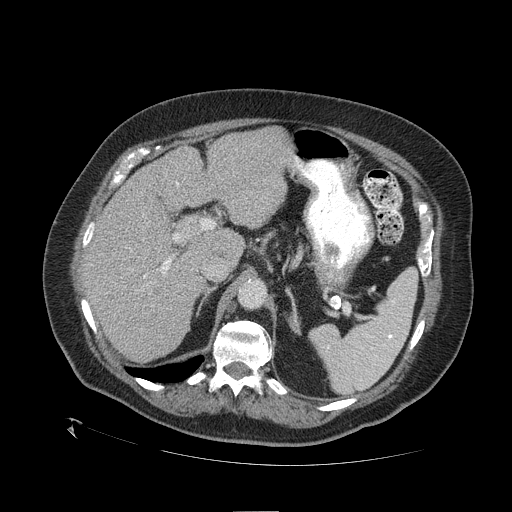
Contrast-enhanced abdominal CT (liver protocol), one axial slice. Slice 72 of 109 in the series (ordered by position). Reconstruction kernel STANDARD. One of 2 acquisitions stored at this slice position. Soft-tissue window (W 400 / L 40 HU). 2.5 mm slice thickness. 512 × 512 image matrix, field of view 460 × 460 mm. From the clinical record (not read from this slice): diagnosis: hepatocellular carcinoma (patient treated with transarterial chemoembolisation; whether this scan precedes or follows treatment is not stated here); TNM stage (as recorded): Stage-I; Child-Pugh class: A; tumour size: 4.6 cm.
Annotated regions visible in this slice (semi-automatically segmented with operator editing):
- liver parenchyma outside the tumour (the mass and vessels are separate outlines, so this box may not span the whole liver): bounding box (x1, y1, x2, y2) in pixels: (82, 128, 292, 362)
- mass: (176, 217, 202, 243)
- liver vessels: (92, 182, 179, 278)